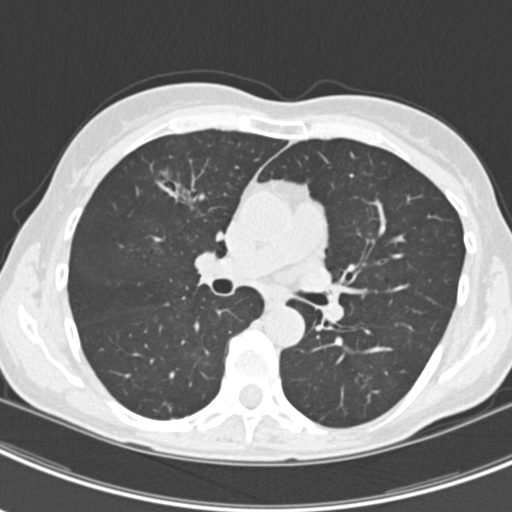
Chest CT (low-dose screening protocol), one axial image; second screening round (one year after baseline); lung window (W 1500 / L -600 HU); 2 mm slice thickness; 120 kVp; slice 83 of 219 in the series; 512 × 512 image matrix, field of view 298 × 298 mm. Female participant, aged 63 years at enrolment.
Lesion marked by an expert reader, bounding box <156,163,215,217> (left, top, right, bottom; pixels). The screening reader recorded 9 non-calcified nodules or masses ≥4 mm on this exam (left upper lobe, right upper lobe, left upper lobe, left lower lobe, right middle lobe, left lower lobe, left lower lobe, right lower lobe, right lower lobe); which of them this box marks is not recorded. Official screen result: positive, other. Lung cancer was diagnosed 408 days after this screen (after the third annual screen): bronchiolo-alveolar adenocarcinoma, NOS, right upper lobe, right middle lobe, right lower lobe, left upper lobe, left lower lobe, moderately differentiated (G2), stage IV (AJCC 6th edition).